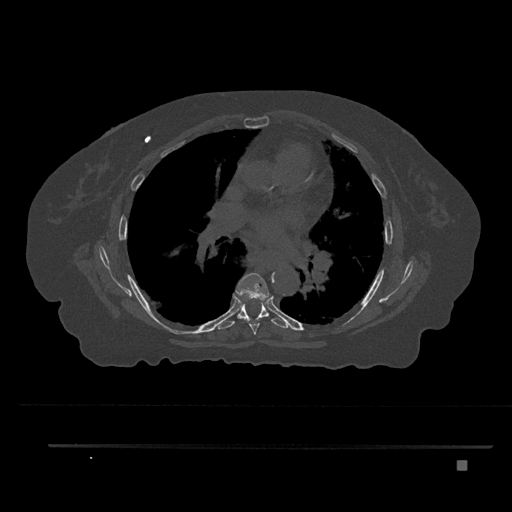
CT including the spine, one axial slice. Slice 506 of 797 in the series (ordered by position). 120 kVp. Bone window (W 1800 / L 400 HU). 0.5 mm slice thickness. 512 × 512 image matrix, field of view 437 × 437 mm. Female patient, age 76 years. From the clinical record (not read from this slice): primary cancer: lung.
Annotated regions visible in this slice (semi-automatic segmentation, software-assisted and operator-edited):
- T6 vertebra: box from (x=234, y=273) to (x=270, y=335) px
- T7 vertebra: (x=218, y=303)–(x=290, y=329)